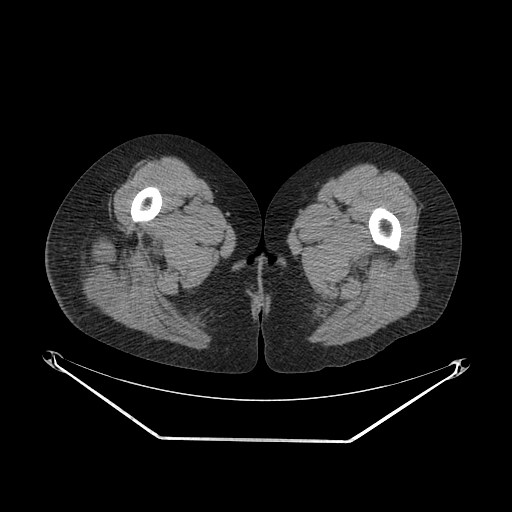
CT of an extremity soft-tissue mass (from a PET/CT study), one axial slice. Slice 25 of 267 in the series (ordered by position). 140 kVp. Soft-tissue window (W 400 / L 40 HU). 3.75 mm slice thickness. 512 × 512 image matrix, field of view 500 × 500 mm. Female patient. From the clinical record (not read from this slice): histological type: epithelioid sarcoma with vascular differentiation; site of the primary tumour: right buttock.
Outlined on this slice (expert contour drawn on MRI and transferred to this co-registered scan by the dataset authors):
- gross tumour volume (mass): box from (x=89, y=247) to (x=117, y=305) px